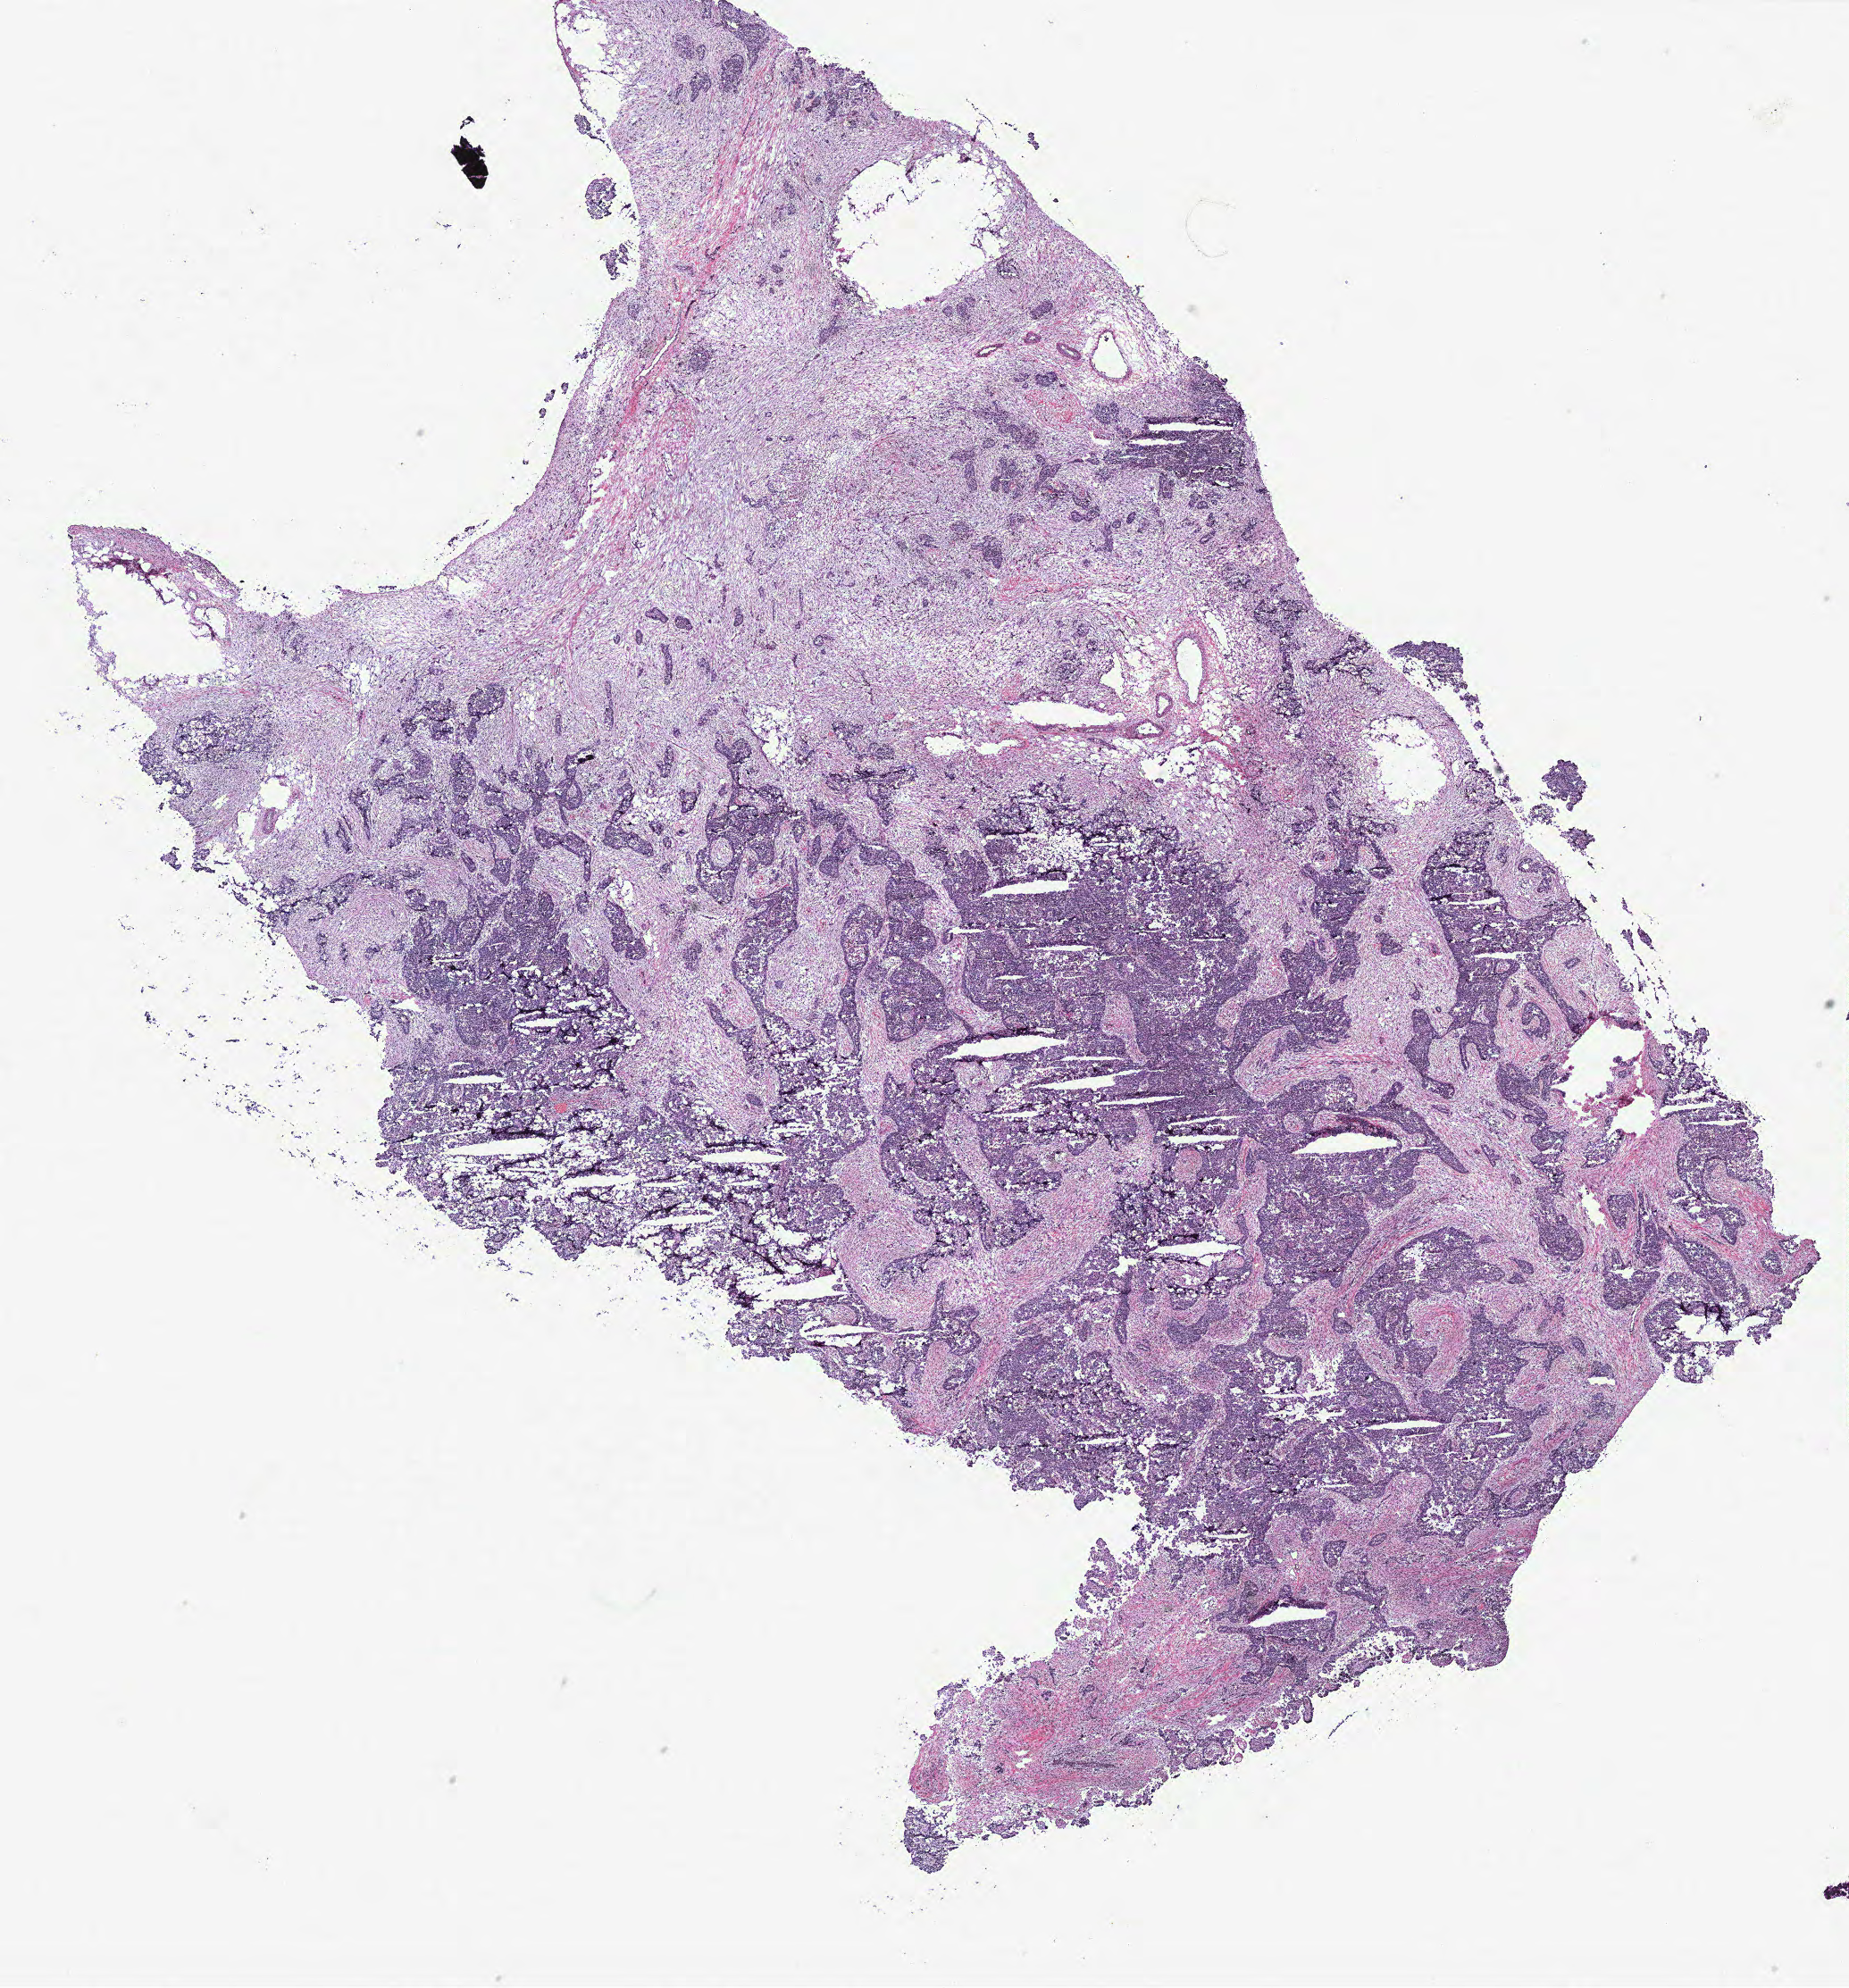
Whole-slide histology image, H&E — a low-resolution overview of the entire scanned area, about 16.6 x 17.8 mm (from a 40x scan). Ovary, tumour tissue. Female, 59 y/o.
Diagnosis: Serous adenocarcinoma, NOS (fallopian tube). Primary tumour site (as recorded): fallopian tube.